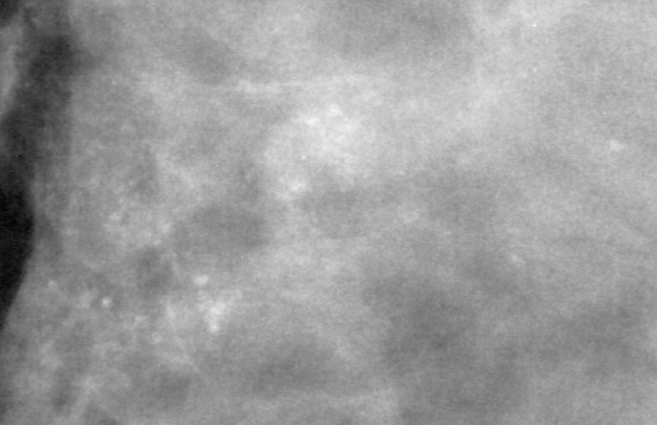
Cropped region of a digitized screen-film mammogram centred on a radiologist-marked abnormality; right breast; CC view; BI-RADS breast density category 4 (scale 1–4).
Calcifications, morphology pleomorphic, distribution segmental; BI-RADS assessment category 4; pathology result (as recorded, not read from the image): benign.